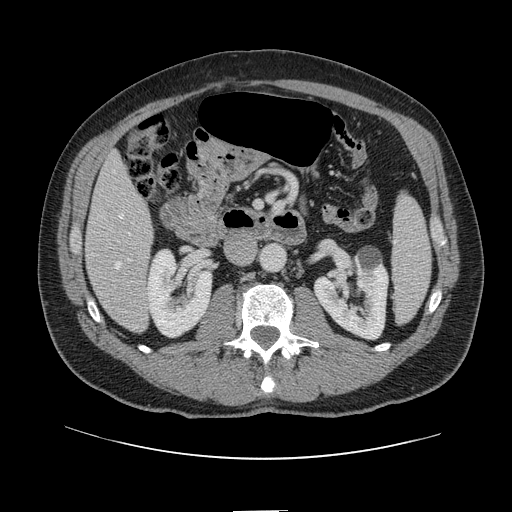
Contrast-enhanced abdominal CT, one axial slice; slice 39 of 161 in the series (ordered by position); 120 kVp; intravenous contrast given; soft-tissue window (W 400 / L 40 HU); 2.5 mm slice thickness; 512 × 512 image matrix, field of view 412 × 412 mm. Male patient, age 66 years. From the clinical record (not read from this slice): diagnosis: colorectal cancer liver metastases, imaged before liver resection; multiple liver metastases: no; largest metastasis: 3.5 cm.
Annotated regions visible in this slice (expert manual segmentation):
- hepatic veins: bounding box (x1, y1, x2, y2) in pixels: (116, 214, 123, 268)
- liver: (87, 156, 153, 332)
- planned liver remnant (the part of the liver to remain after resection): (87, 155, 150, 268)